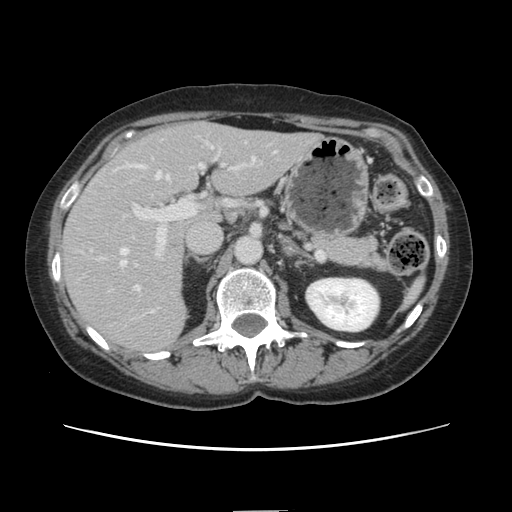
Contrast-enhanced abdominal CT, one axial slice; position 78 of 141 along the scan axis; 120 kVp; intravenous contrast given; soft-tissue window (W 400 / L 40 HU); 2.5 mm slice thickness; 512 × 512 image matrix, field of view 350 × 350 mm. Female patient, age 63 years. Case-level facts recorded for this patient, not image findings: diagnosis: colorectal cancer liver metastases, imaged before liver resection; multiple liver metastases: yes; largest metastasis: 3.2 cm; chemotherapy before resection: yes.
Outlined on this slice (outlined manually by an expert reader):
- hepatic veins: bounding box <119,158,255,268> (left, top, right, bottom; pixels)
- liver: <62,123,316,354>
- planned liver remnant (the part of the liver to remain after resection): <175,122,316,220>
- portal vein (with intrahepatic branches): <132,163,238,312>